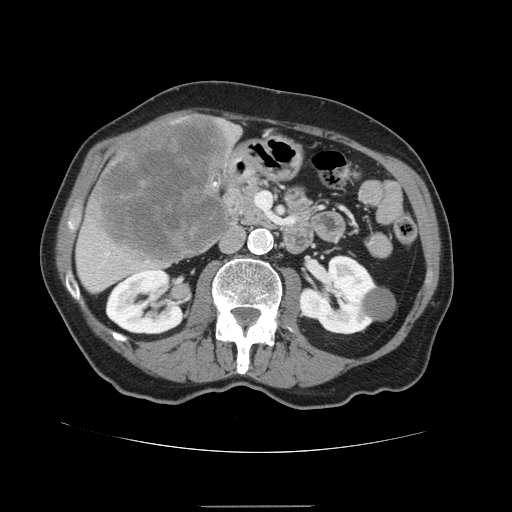
Contrast-enhanced abdominal CT, one axial slice; slice 59 of 168 in the series (ordered by position); intravenous contrast given; soft-tissue window (W 400 / L 40 HU); 2.5 mm slice thickness; 512 × 512 image matrix, field of view 386 × 386 mm. Male patient, age 74 years. From the clinical record (not read from this slice): diagnosis: colorectal cancer liver metastases, imaged before liver resection; multiple liver metastases: no; largest metastasis: 14.5 cm.
Outlined on this slice (manually delineated by an expert):
- liver: bounding box [x1, y1, x2, y2] px = [75, 113, 242, 294]
- liver metastasis: [97, 117, 230, 264]